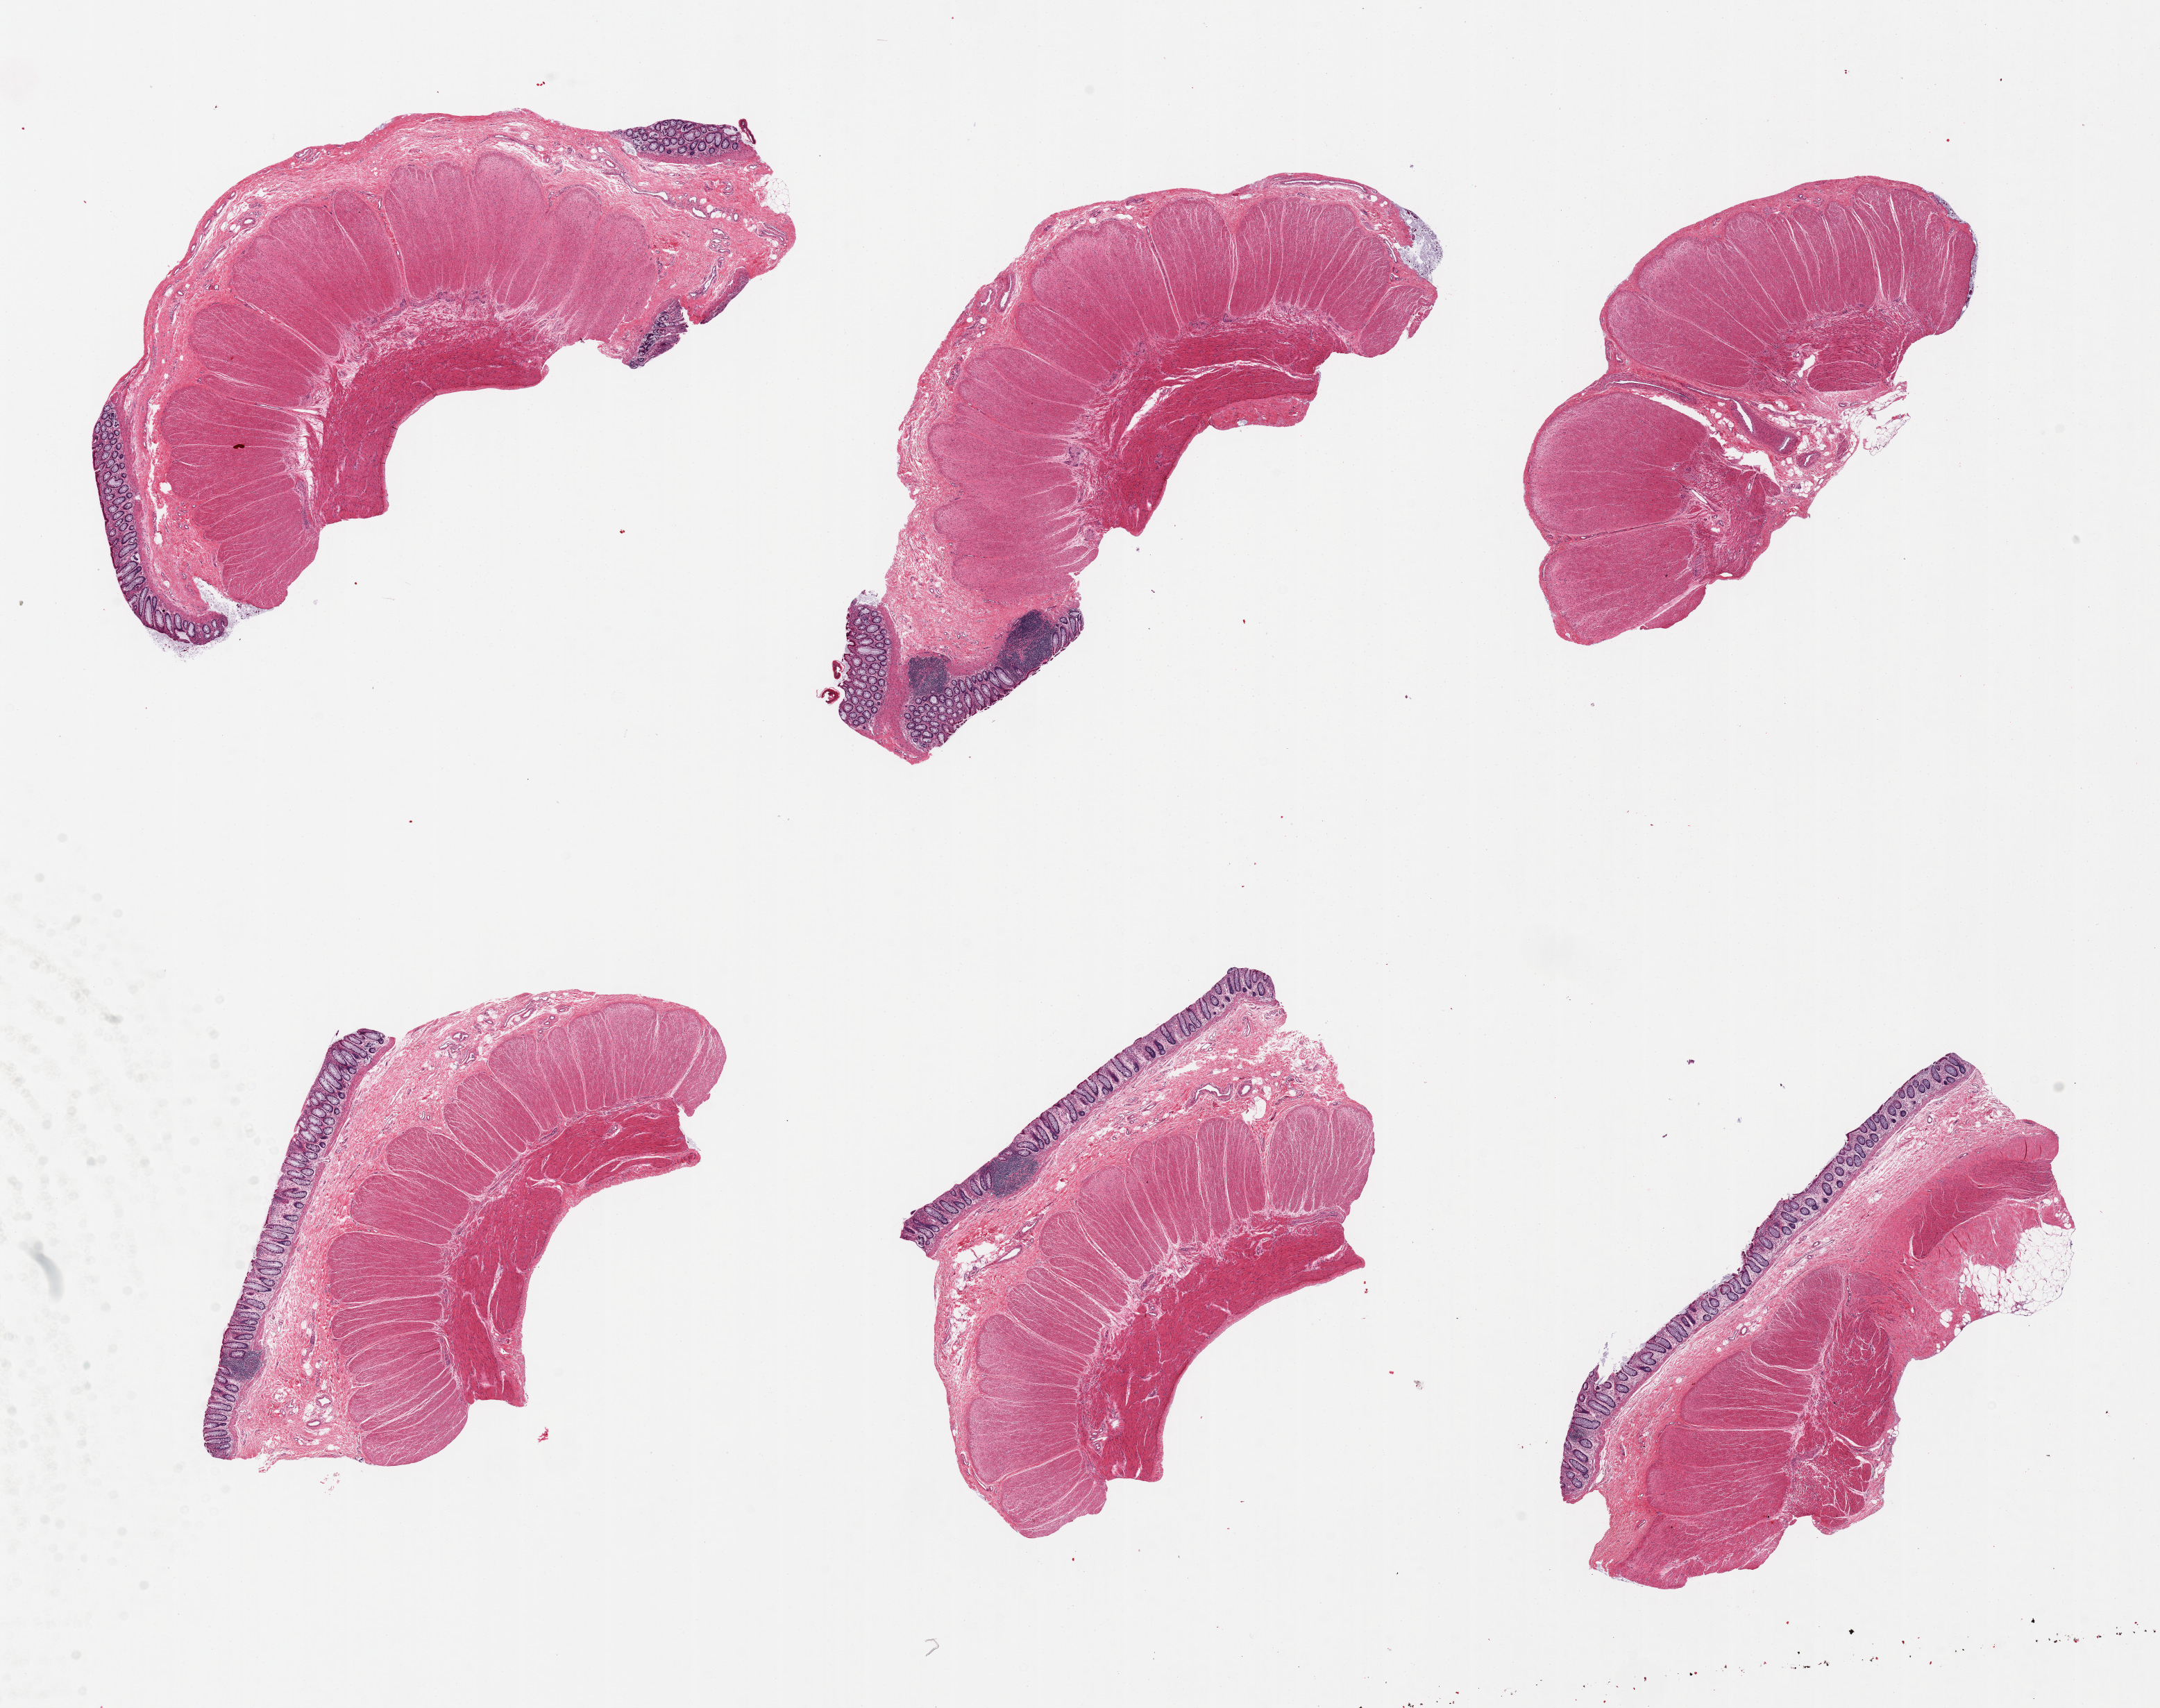
Digitized hematoxylin and eosin (H&E)-stained section, low-resolution overview of the scanned area, about 24.6 x 19.5 mm (from a 20x scan). PAXgene-fixed, paraffin-embedded tissue. Sampled site (target tissue): sigmoid colon. Donor tissue sample. Female donor.
Review note (as recorded): 6 pieces; 5 of 6 pieces with mucosa [not target].